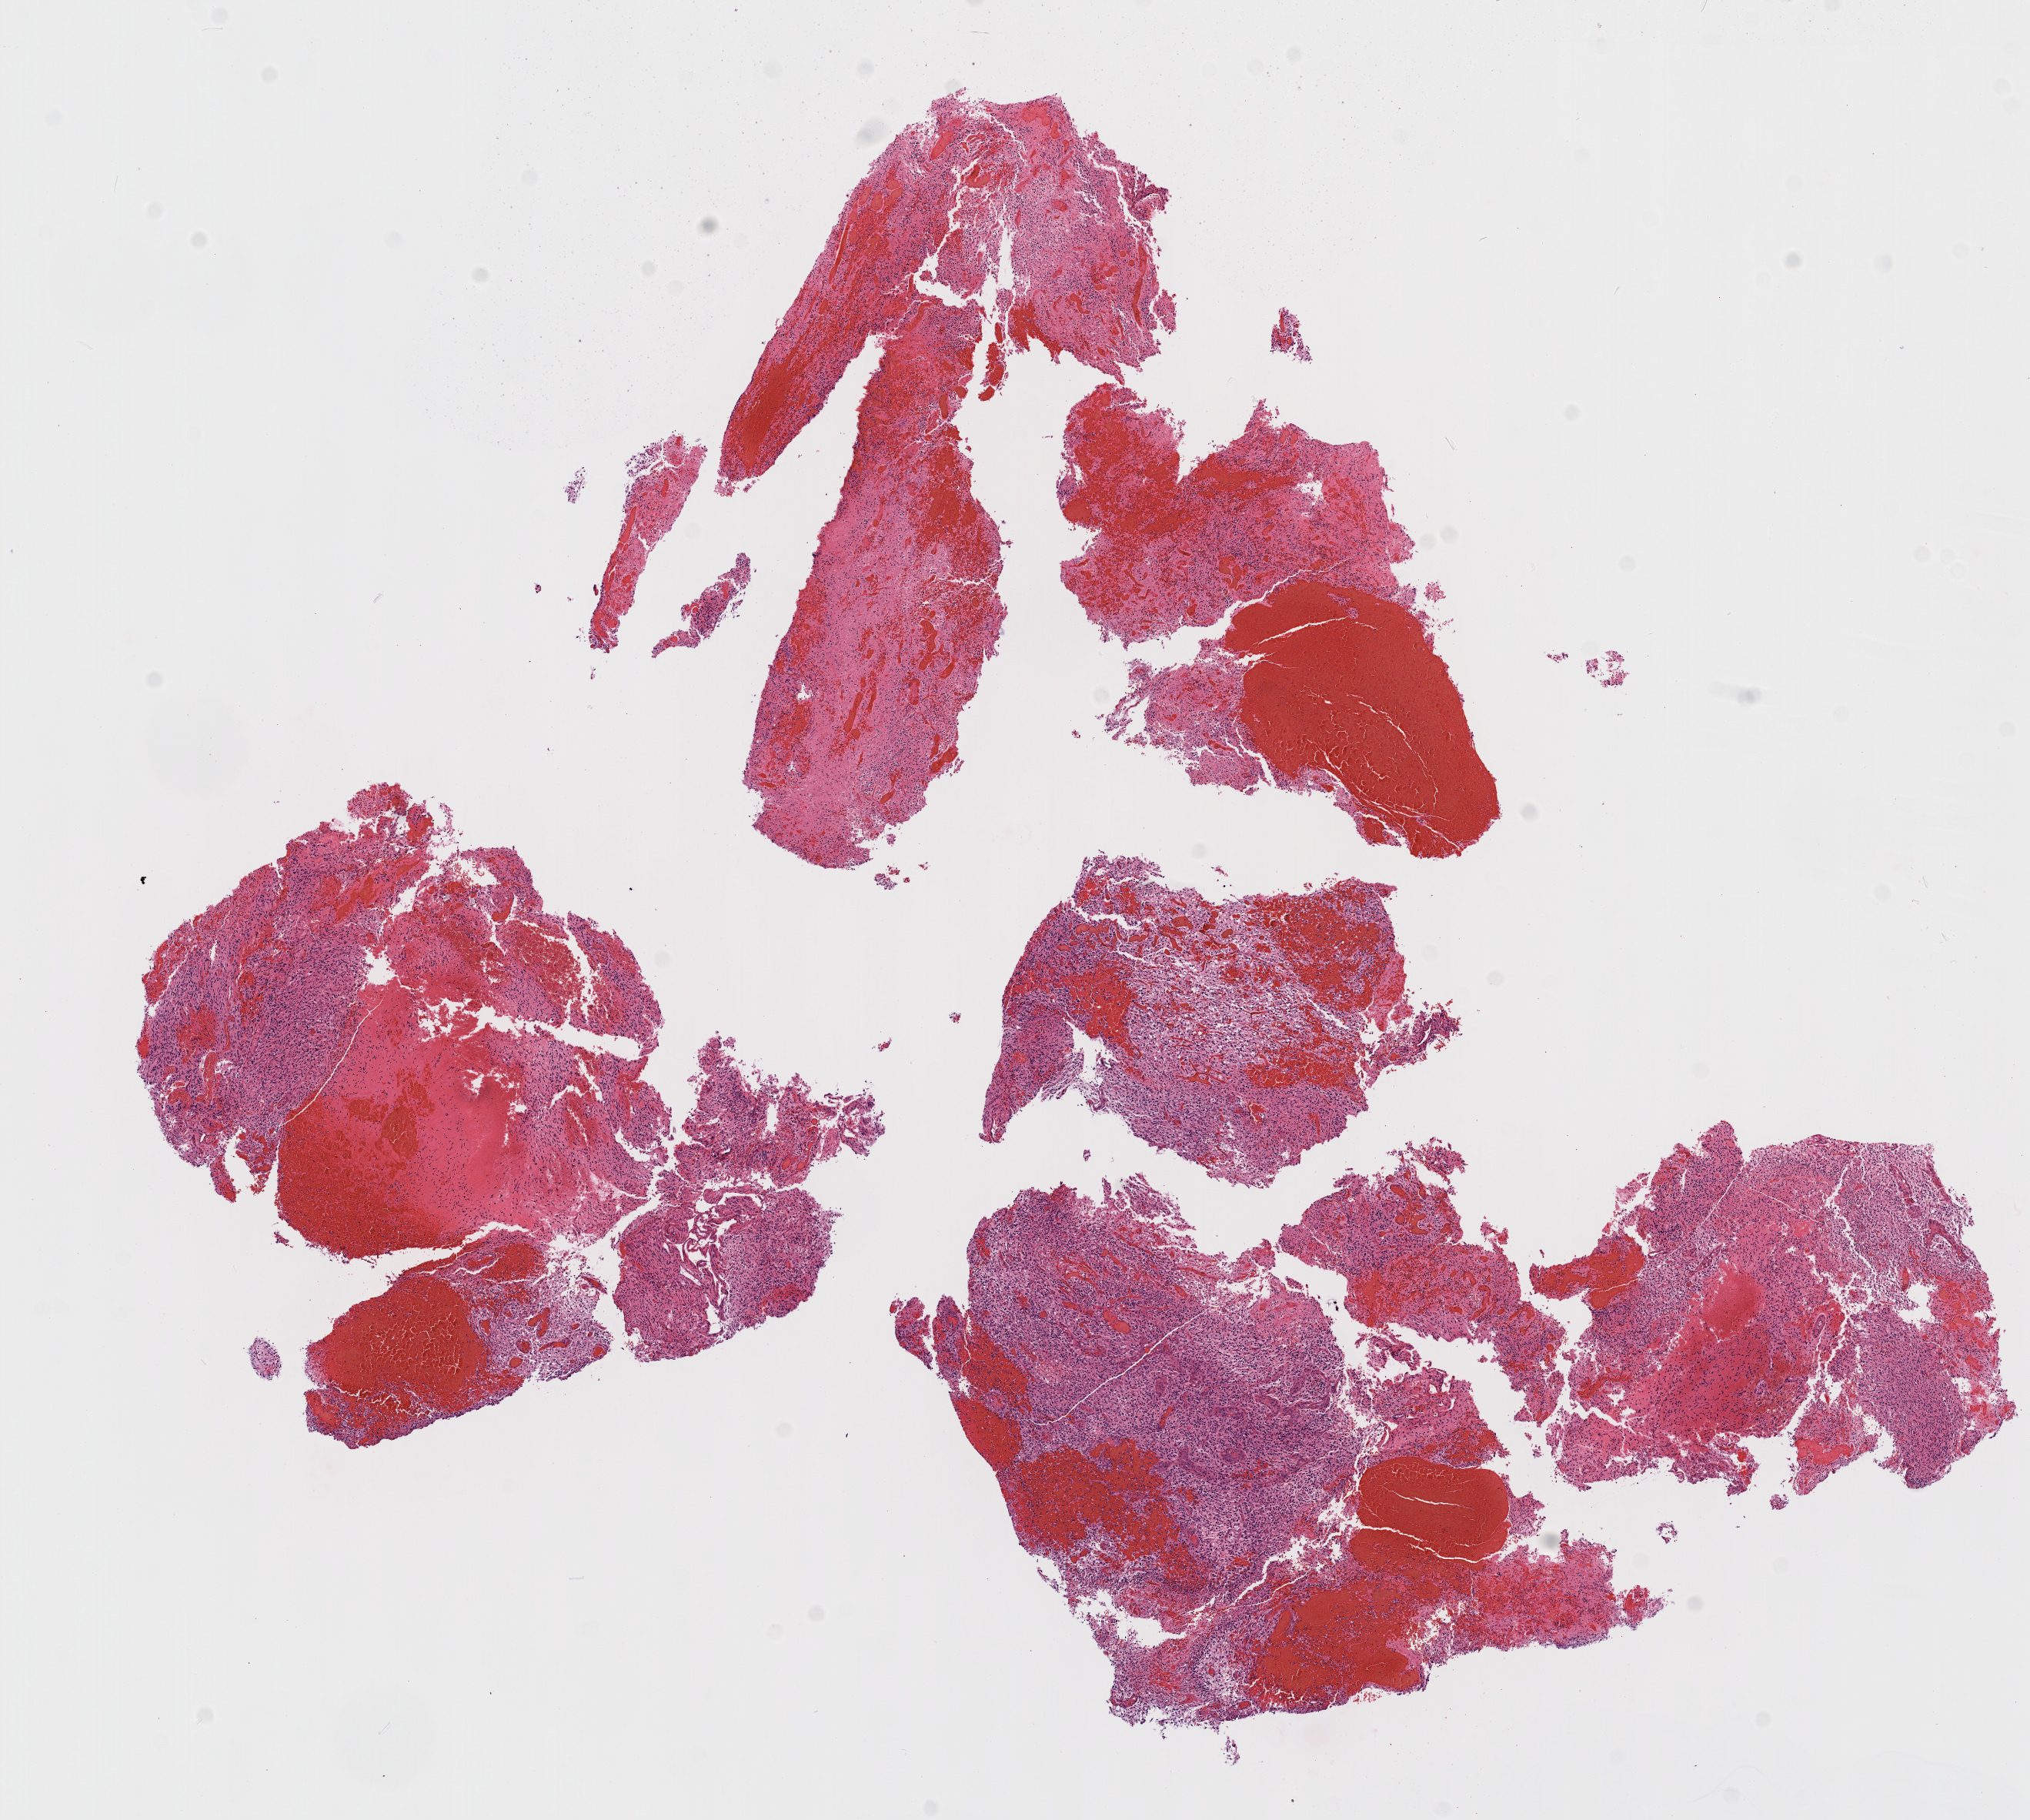
Hematoxylin and eosin (H&E) stained whole-slide image — low-resolution overview of the scanned area, about 10.6 x 9.5 mm (slide scanned at 20x). FFPE section. Sample: primary tumour, brain. Patient: male, age at initial diagnosis 54 years.
Diagnosis: Glioblastoma.